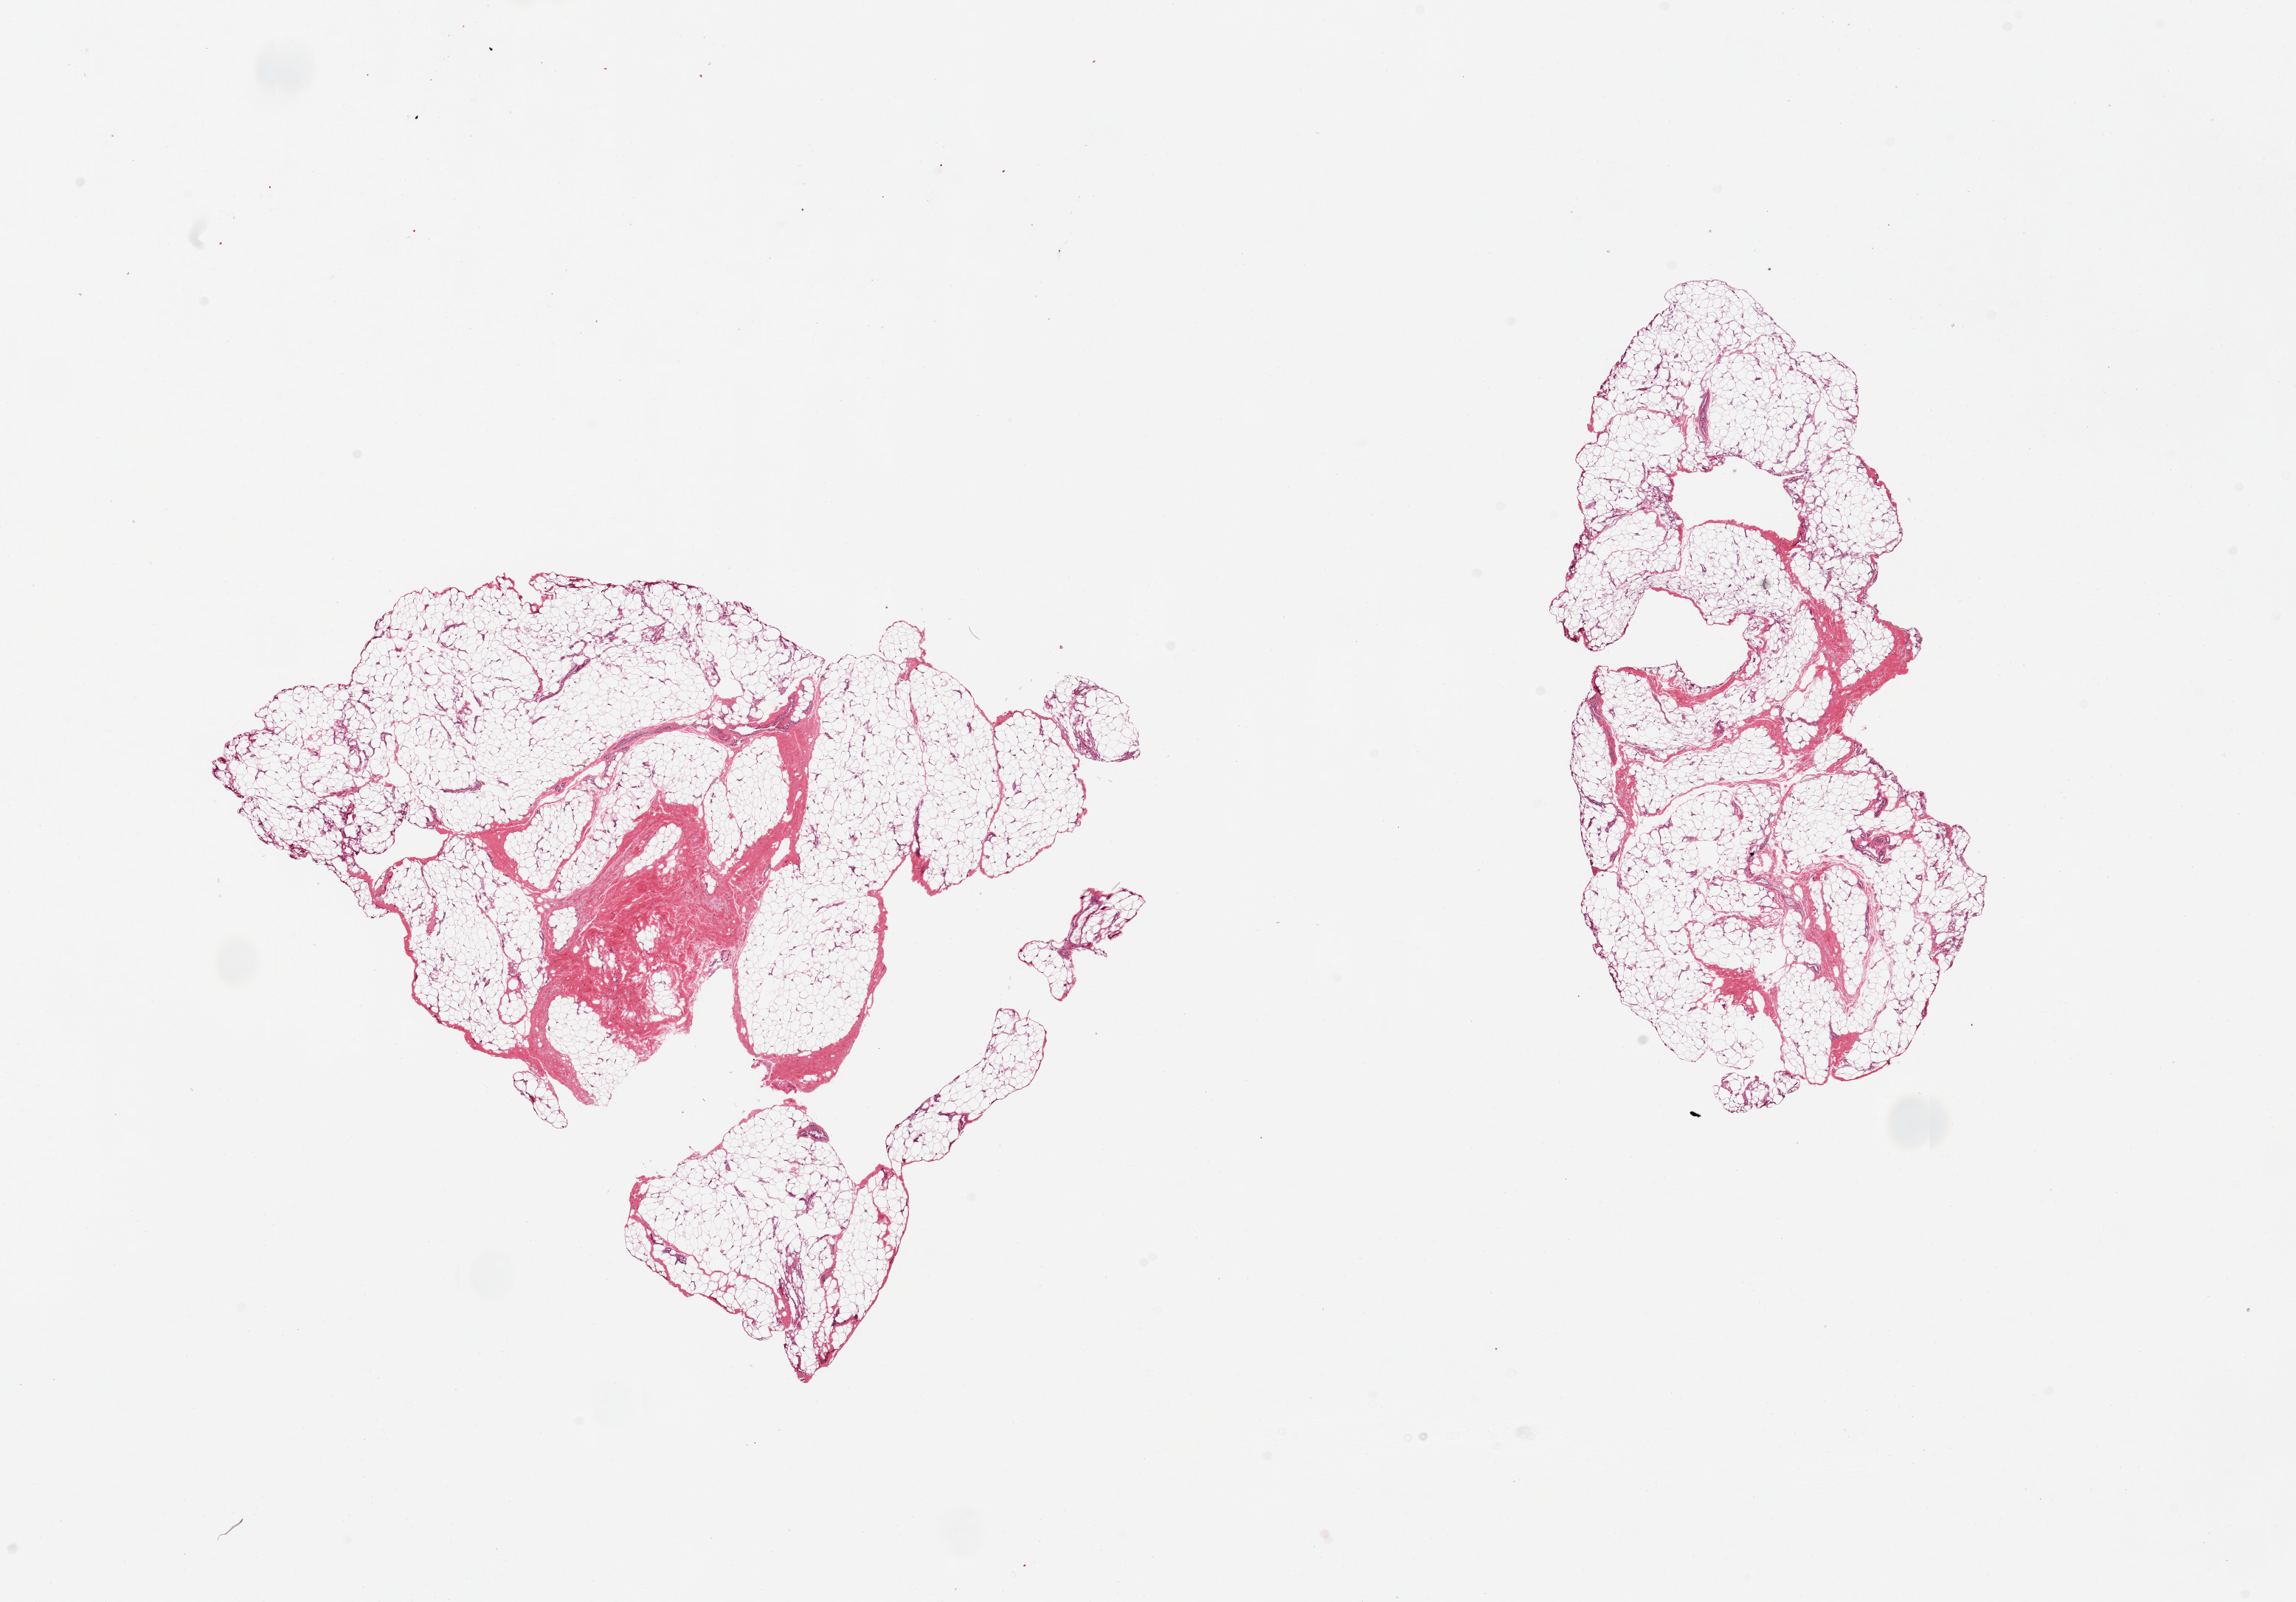
H&E whole-slide image, a low-resolution overview of the entire scanned area, about 24.6 x 17.2 mm, PAXgene-fixed paraffin-embedded (PFPE) section, target tissue: adipose tissue, tissue donor sample. Donor sex: male.
Review note (as recorded): 2 pieces, ~15-20% fascia.